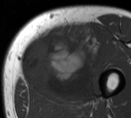
MRI of an extremity soft-tissue mass, one axial slice. Position 25 of 55 along the scan axis. MR volume resampled by the dataset authors to the PET/CT grid (not the native acquisition matrix). 131 × 118 image matrix, field of view 128 × 115 mm. Male patient. Case-level facts recorded for this patient, not image findings: histological type: pleiomorphic liposarcoma; grade: high; site of the primary tumour: left thigh.
Structures marked on this image (expert contour drawn on MRI and transferred to this co-registered scan by the dataset authors):
- gross tumour volume including surrounding oedema: bounding box <18,23,104,102> (left, top, right, bottom; pixels)
- gross tumour volume (mass): <20,27,95,102>